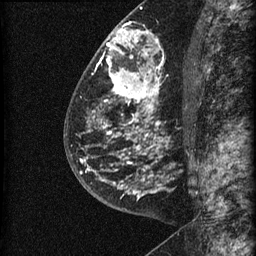
Breast MRI (dynamic contrast-enhanced), one sagittal slice; slice 35 of 60 in the series (ordered by position); dynamic contrast-enhanced series, image 2 of 3 at this slice position (ordered by acquisition); 1.5 T; TE 4.2 ms, TR 22.7 ms; 1.5 mm slice thickness; 256 × 256 image matrix. Female patient, age 48 years. From the clinical record (not read from this slice): setting: breast cancer imaged before/during neoadjuvant chemotherapy; receptor status: triple-negative.
Annotated regions visible in this slice (semi-automatic segmentation, software-assisted and operator-edited):
- analysis volume of interest (the breast-tissue region the enhancement analysis was run in; not a lesion): bounding box <81,23,186,202> (left, top, right, bottom; pixels)
- tumour enhancement mask (voxels above the 90 % enhancement threshold inside the analysis volume of interest): <81,29,164,197>